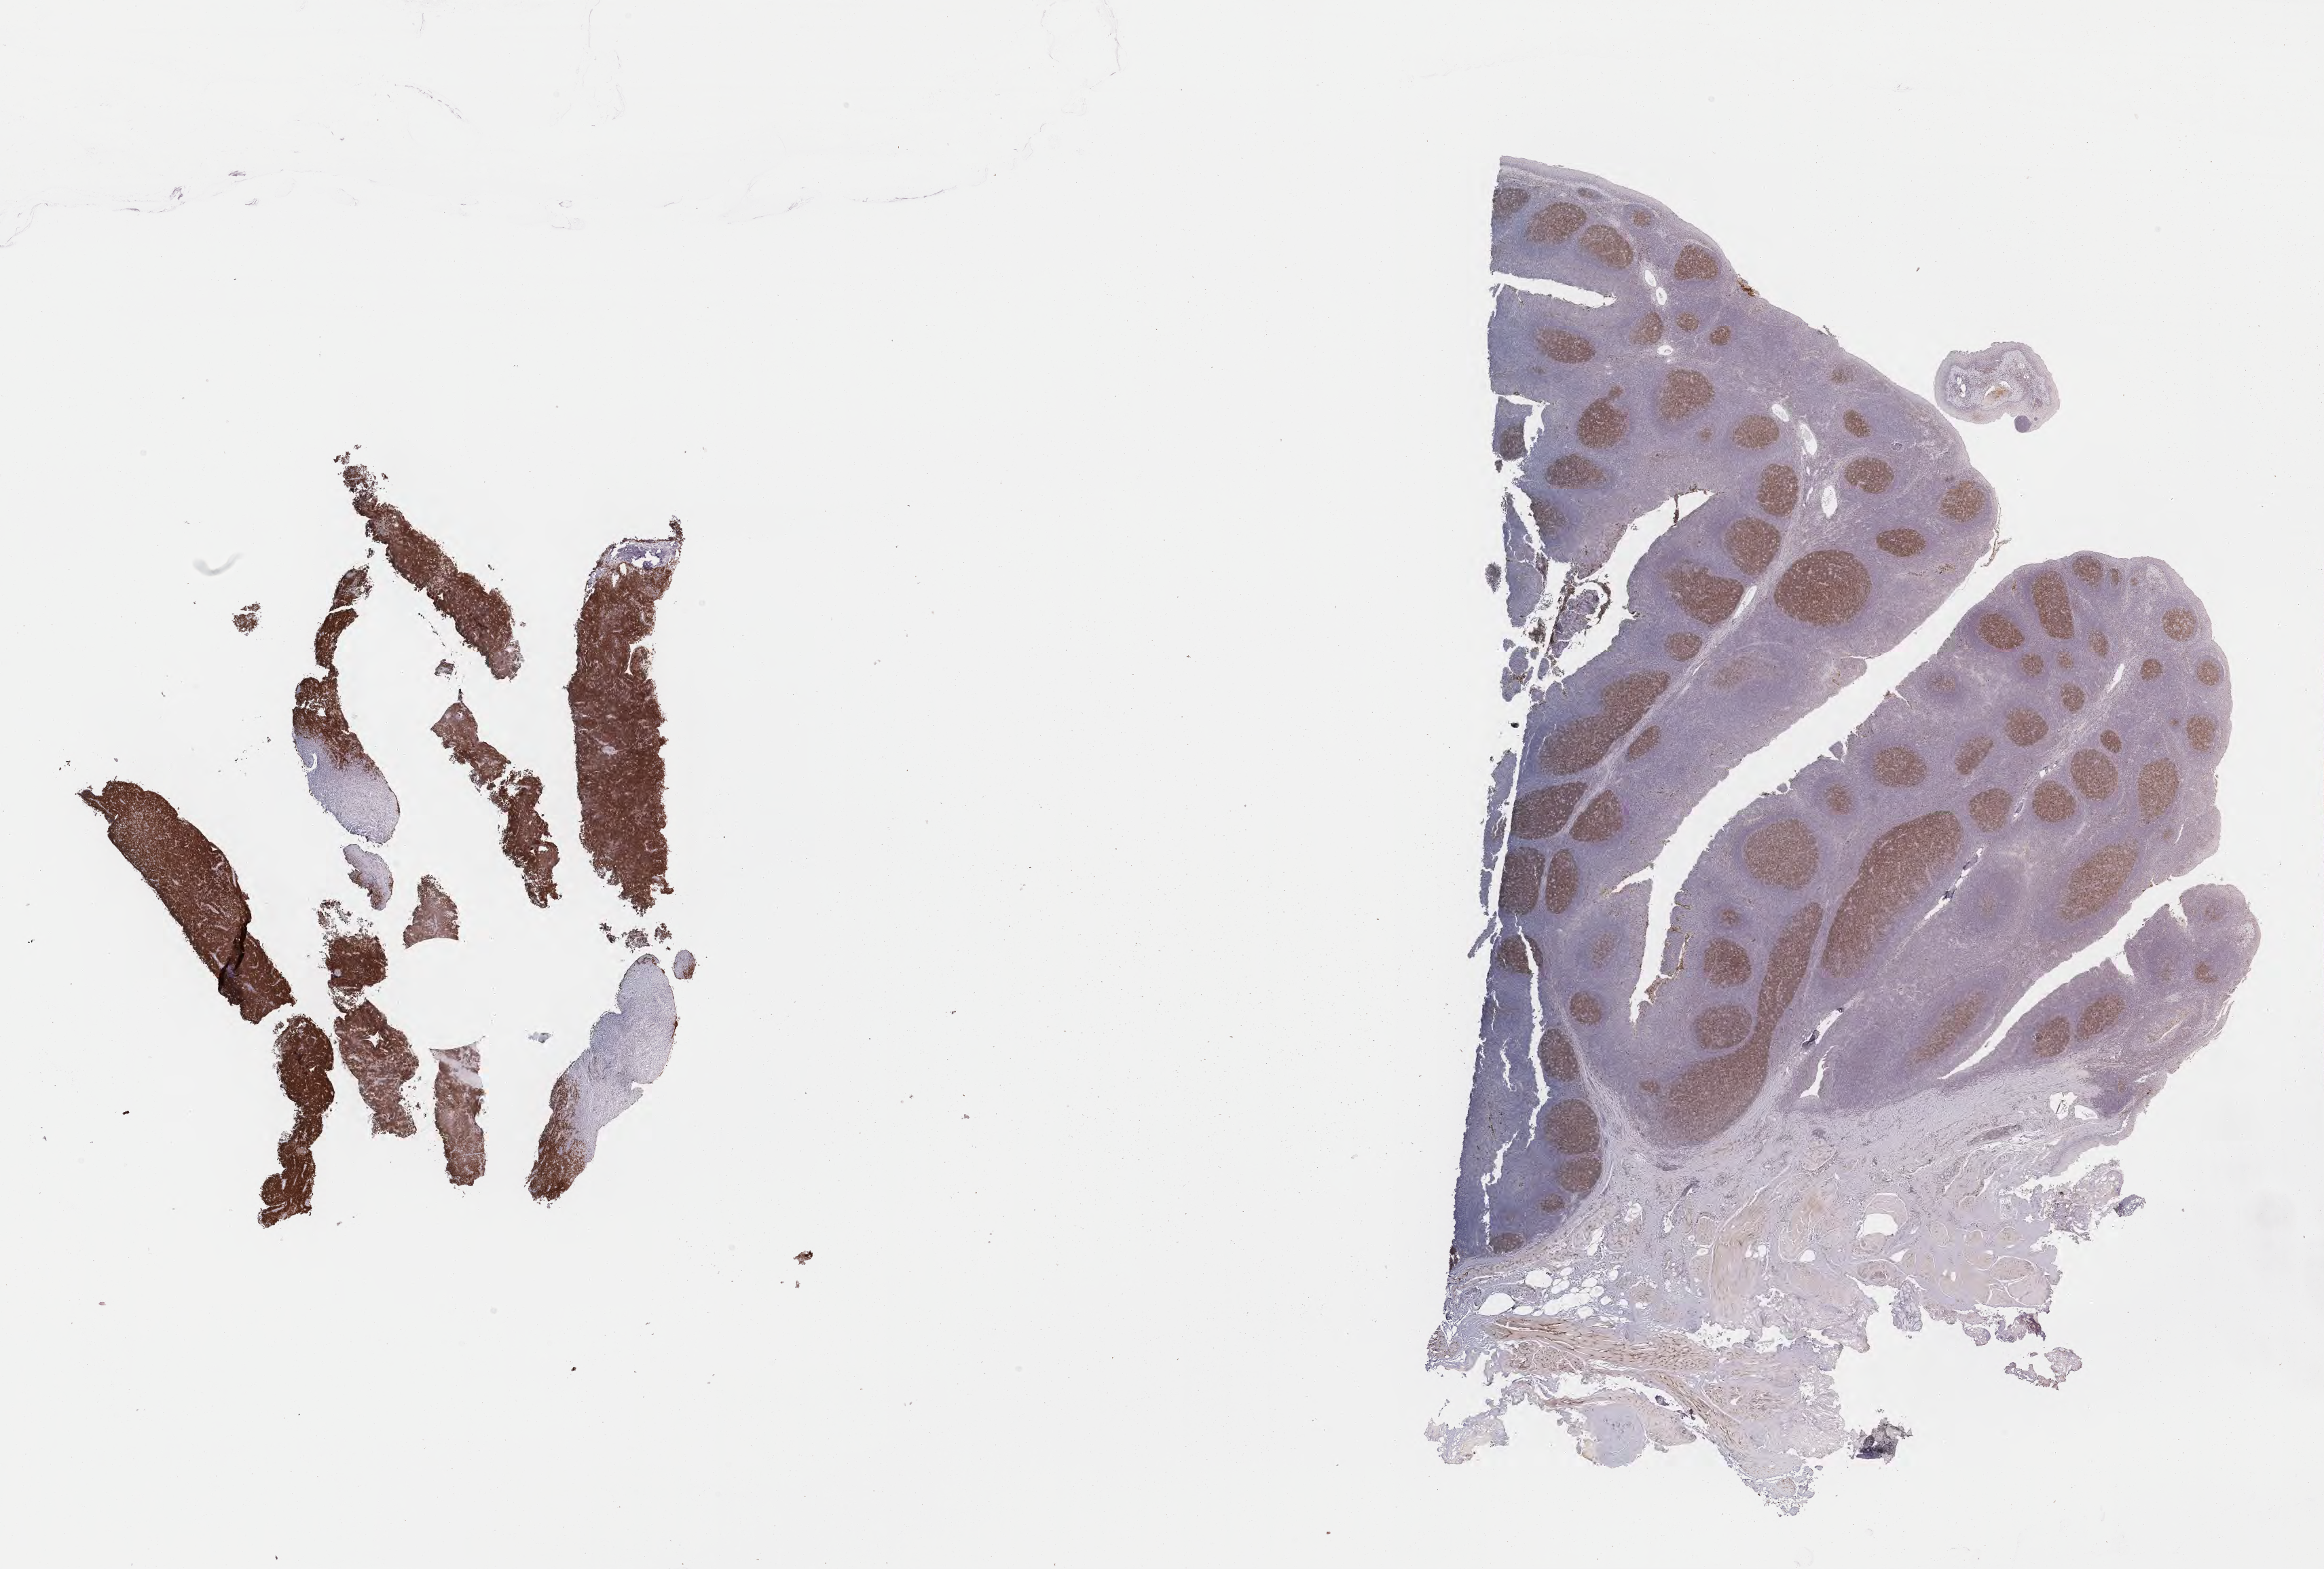
IHC for CD10, whole-slide image — shown as a low-resolution overview of the whole scanned area (about 27.7 x 18.7 mm), tumor tissue, anatomic site: abdomen proper. Male, age 7 years at initial diagnosis.
* histologic diagnosis: Burkitt lymphoma, NOS